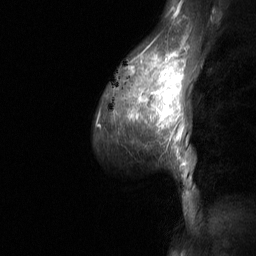
Breast MRI (dynamic contrast-enhanced), one sagittal slice. Position 48 of 64 along the scan axis. Dynamic contrast-enhanced study with each time point stored as its own series, time point 2 of 3 at this slice position (early post-contrast, ordered by acquisition time). 1.5 T. TE 4.8 ms, TR 27 ms. 2 mm slice thickness. 256 × 256 image matrix, field of view 200 × 200 mm. Female patient, age 36 years. Case-level facts recorded for this patient, not image findings: setting: breast cancer imaged before/during neoadjuvant chemotherapy; receptor status: HR-positive, HER2-negative.
Outlined on this slice (semi-automatically segmented with operator editing):
- analysis volume of interest (the breast-tissue region the enhancement analysis was run in; not a lesion): bounding box <95,45,187,210> (left, top, right, bottom; pixels)
- tumour enhancement mask (voxels above the 90 % enhancement threshold inside the analysis volume of interest): <129,51,185,142>